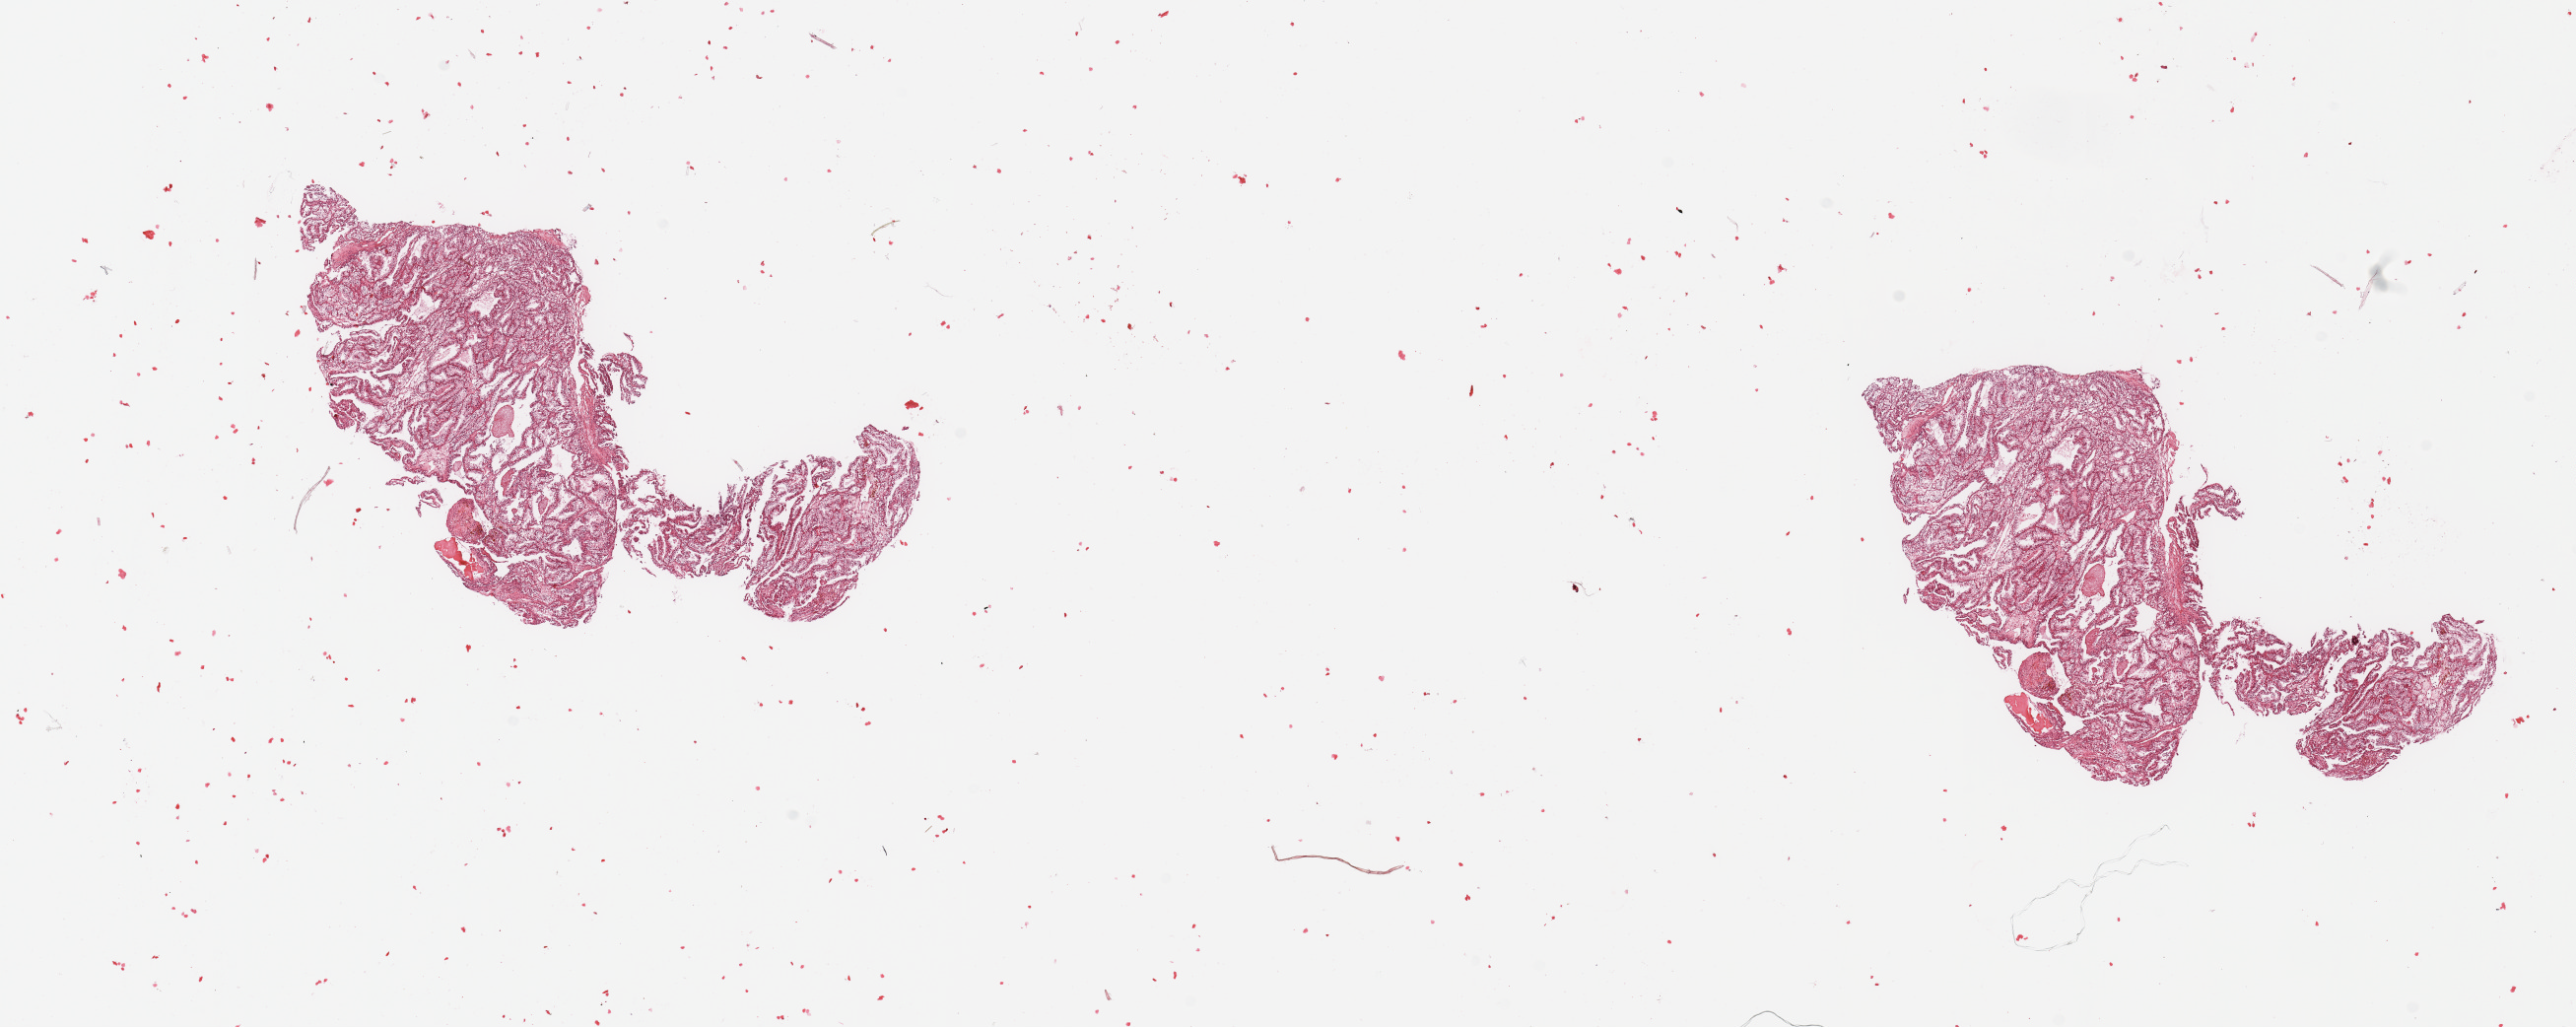
Hematoxylin and eosin (H&E) stained whole-slide image — low-resolution overview of the scanned area, about 20.7 x 8.2 mm (from a 20x scan), tumour tissue sample, sampled site: kidney. Male, 52 y/o. Histologic grade: G2 (moderately differentiated). Pathologist review of this section (percent, as recorded): tumour nuclei 85%, necrosis 5%.
Primary tumour site (as recorded): upper pole. Histologic diagnosis: Renal cell carcinoma, NOS. AJCC pathologic stage: II.